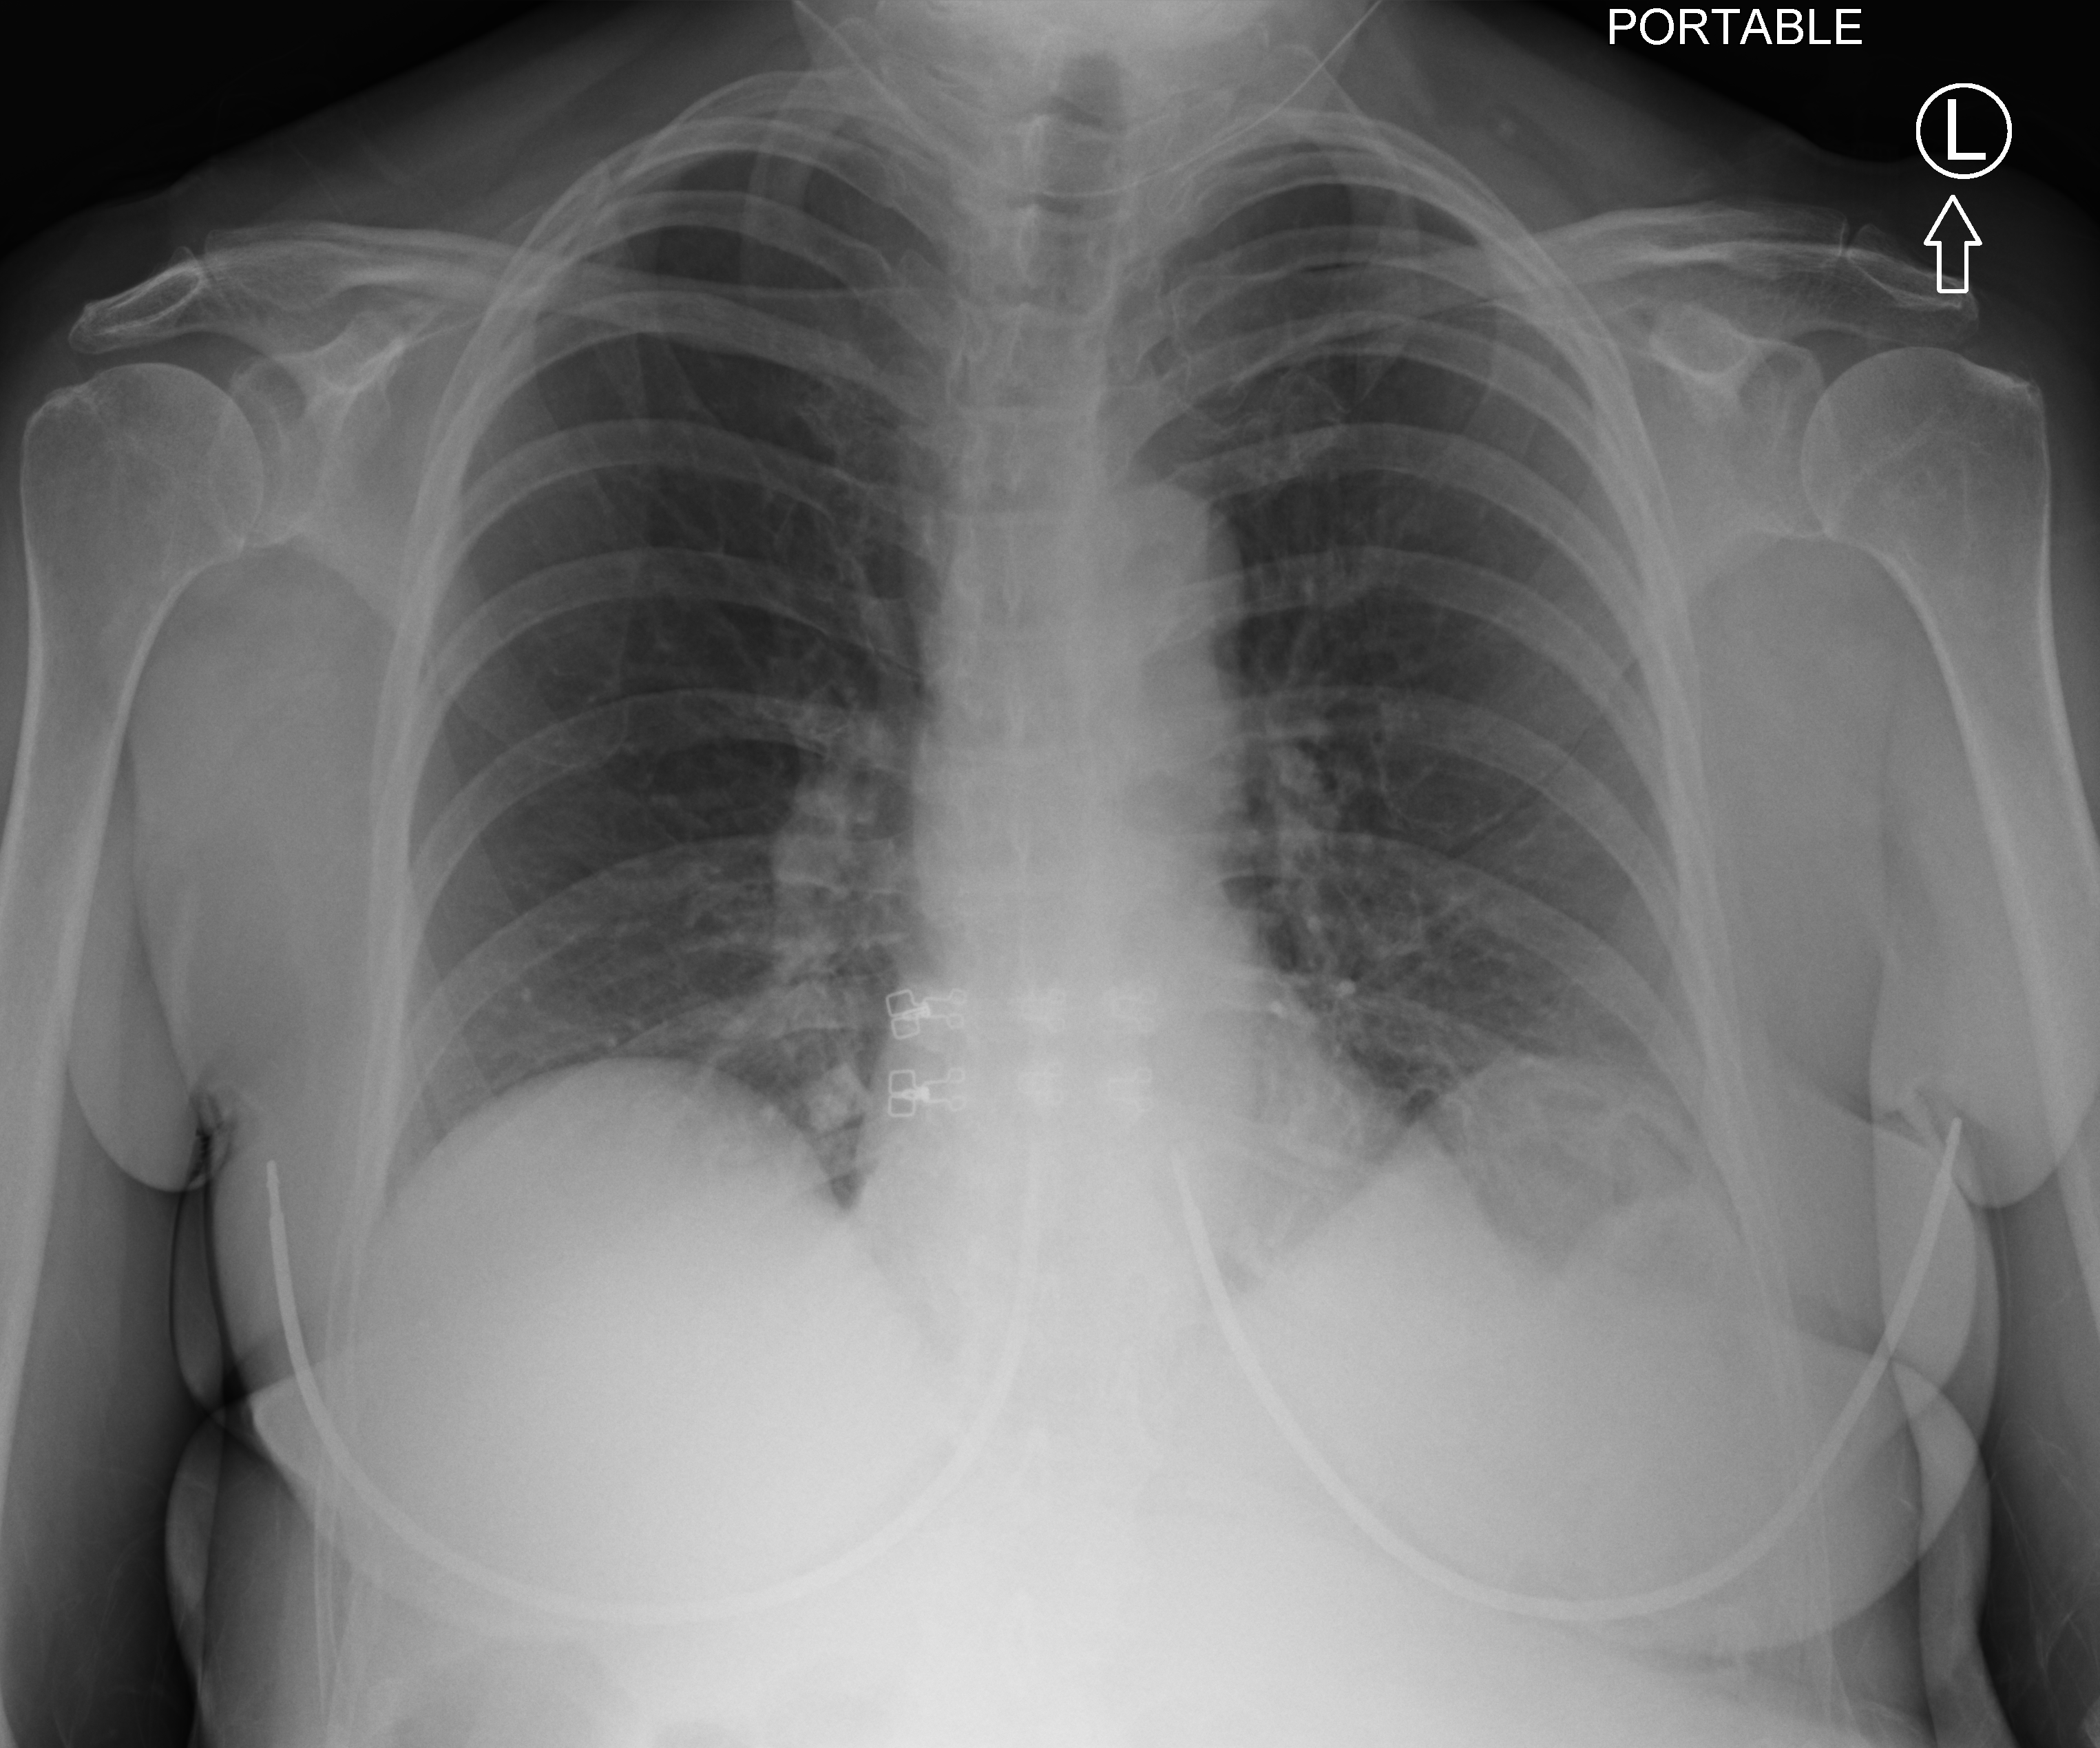
Bedside chest radiograph (computed radiography); anteroposterior (AP) projection. Patient hospitalised with COVID-19; female, aged 75–90 years.
Admission-level facts for this patient (not findings on this image; timing relative to this image not recorded): hypertension (admission record): yes; smoking status (admission record): never.